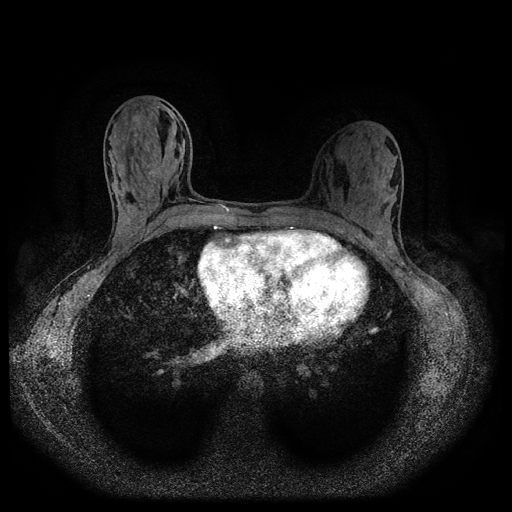
Breast MRI (dynamic contrast-enhanced, multi-phase), one axial slice; position 48 of 116 along the scan axis; dynamic contrast-enhanced series, time point 2 of 5 at this slice position (early post-contrast); 1.5 T; TE 2.7 ms, TR 5.4 ms; 2 mm slice thickness; 512 × 512 image matrix, field of view 330 × 330 mm. Female patient, age 32 years.
Structures marked on this image (semi-automatically segmented with operator editing):
- breast lesion (labelled benign in the annotation): bounding box <128,115,142,141> (left, top, right, bottom; pixels)